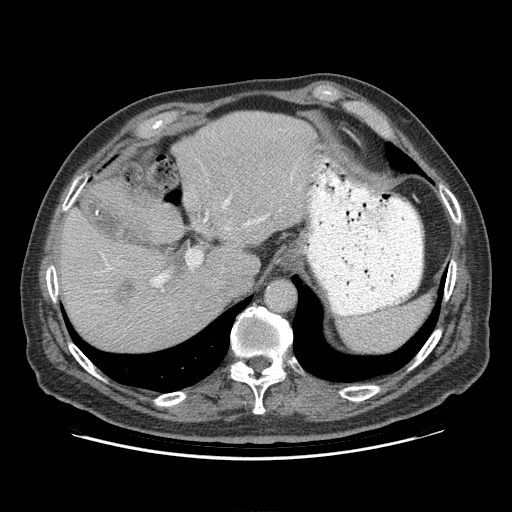
Contrast-enhanced abdominal CT (liver protocol), one axial slice. Position 69 of 95 along the scan axis. Reconstruction kernel STANDARD. Soft-tissue window (W 400 / L 40 HU). 2.5 mm slice thickness. 512 × 512 image matrix. From the clinical record (not read from this slice): diagnosis: hepatocellular carcinoma (patient treated with transarterial chemoembolisation; whether this scan precedes or follows treatment is not stated here); TNM stage (as recorded): Stage-IVB; Child-Pugh class: A; tumour differentiation: well differentiated.
Structures marked on this image (semi-automatic segmentation, software-assisted and operator-edited):
- abdominal aorta: box from (x=266, y=280) to (x=294, y=311) px
- liver parenchyma outside the tumour (the mass and vessels are separate outlines, so this box may not span the whole liver): (x=60, y=110)–(x=325, y=352)
- mass: (x=108, y=278)–(x=138, y=311)
- liver vessels: (x=152, y=178)–(x=292, y=287)